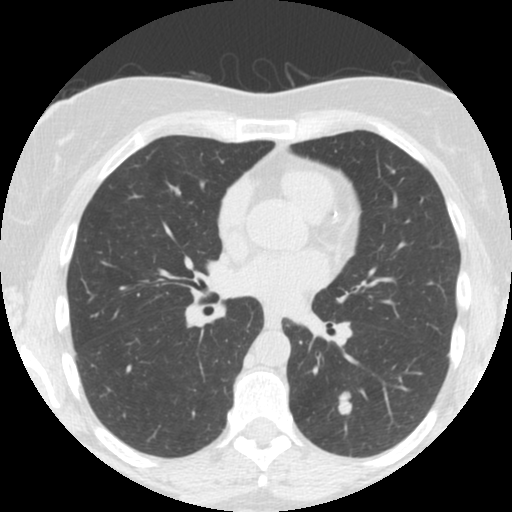
Low-dose screening chest CT, one axial slice. Position 79 of 150 along the scan axis. Reconstruction kernel STANDARD. Lung window (W 1500 / L -600 HU). 2.5 mm slice thickness. 512 × 512 image matrix, field of view 300 × 300 mm.
Structures marked on this image (manually delineated by an expert):
- lesion 1 (tumor, lower lobe of left lung): bounding box (x1, y1, x2, y2) in pixels: (338, 392, 352, 415)